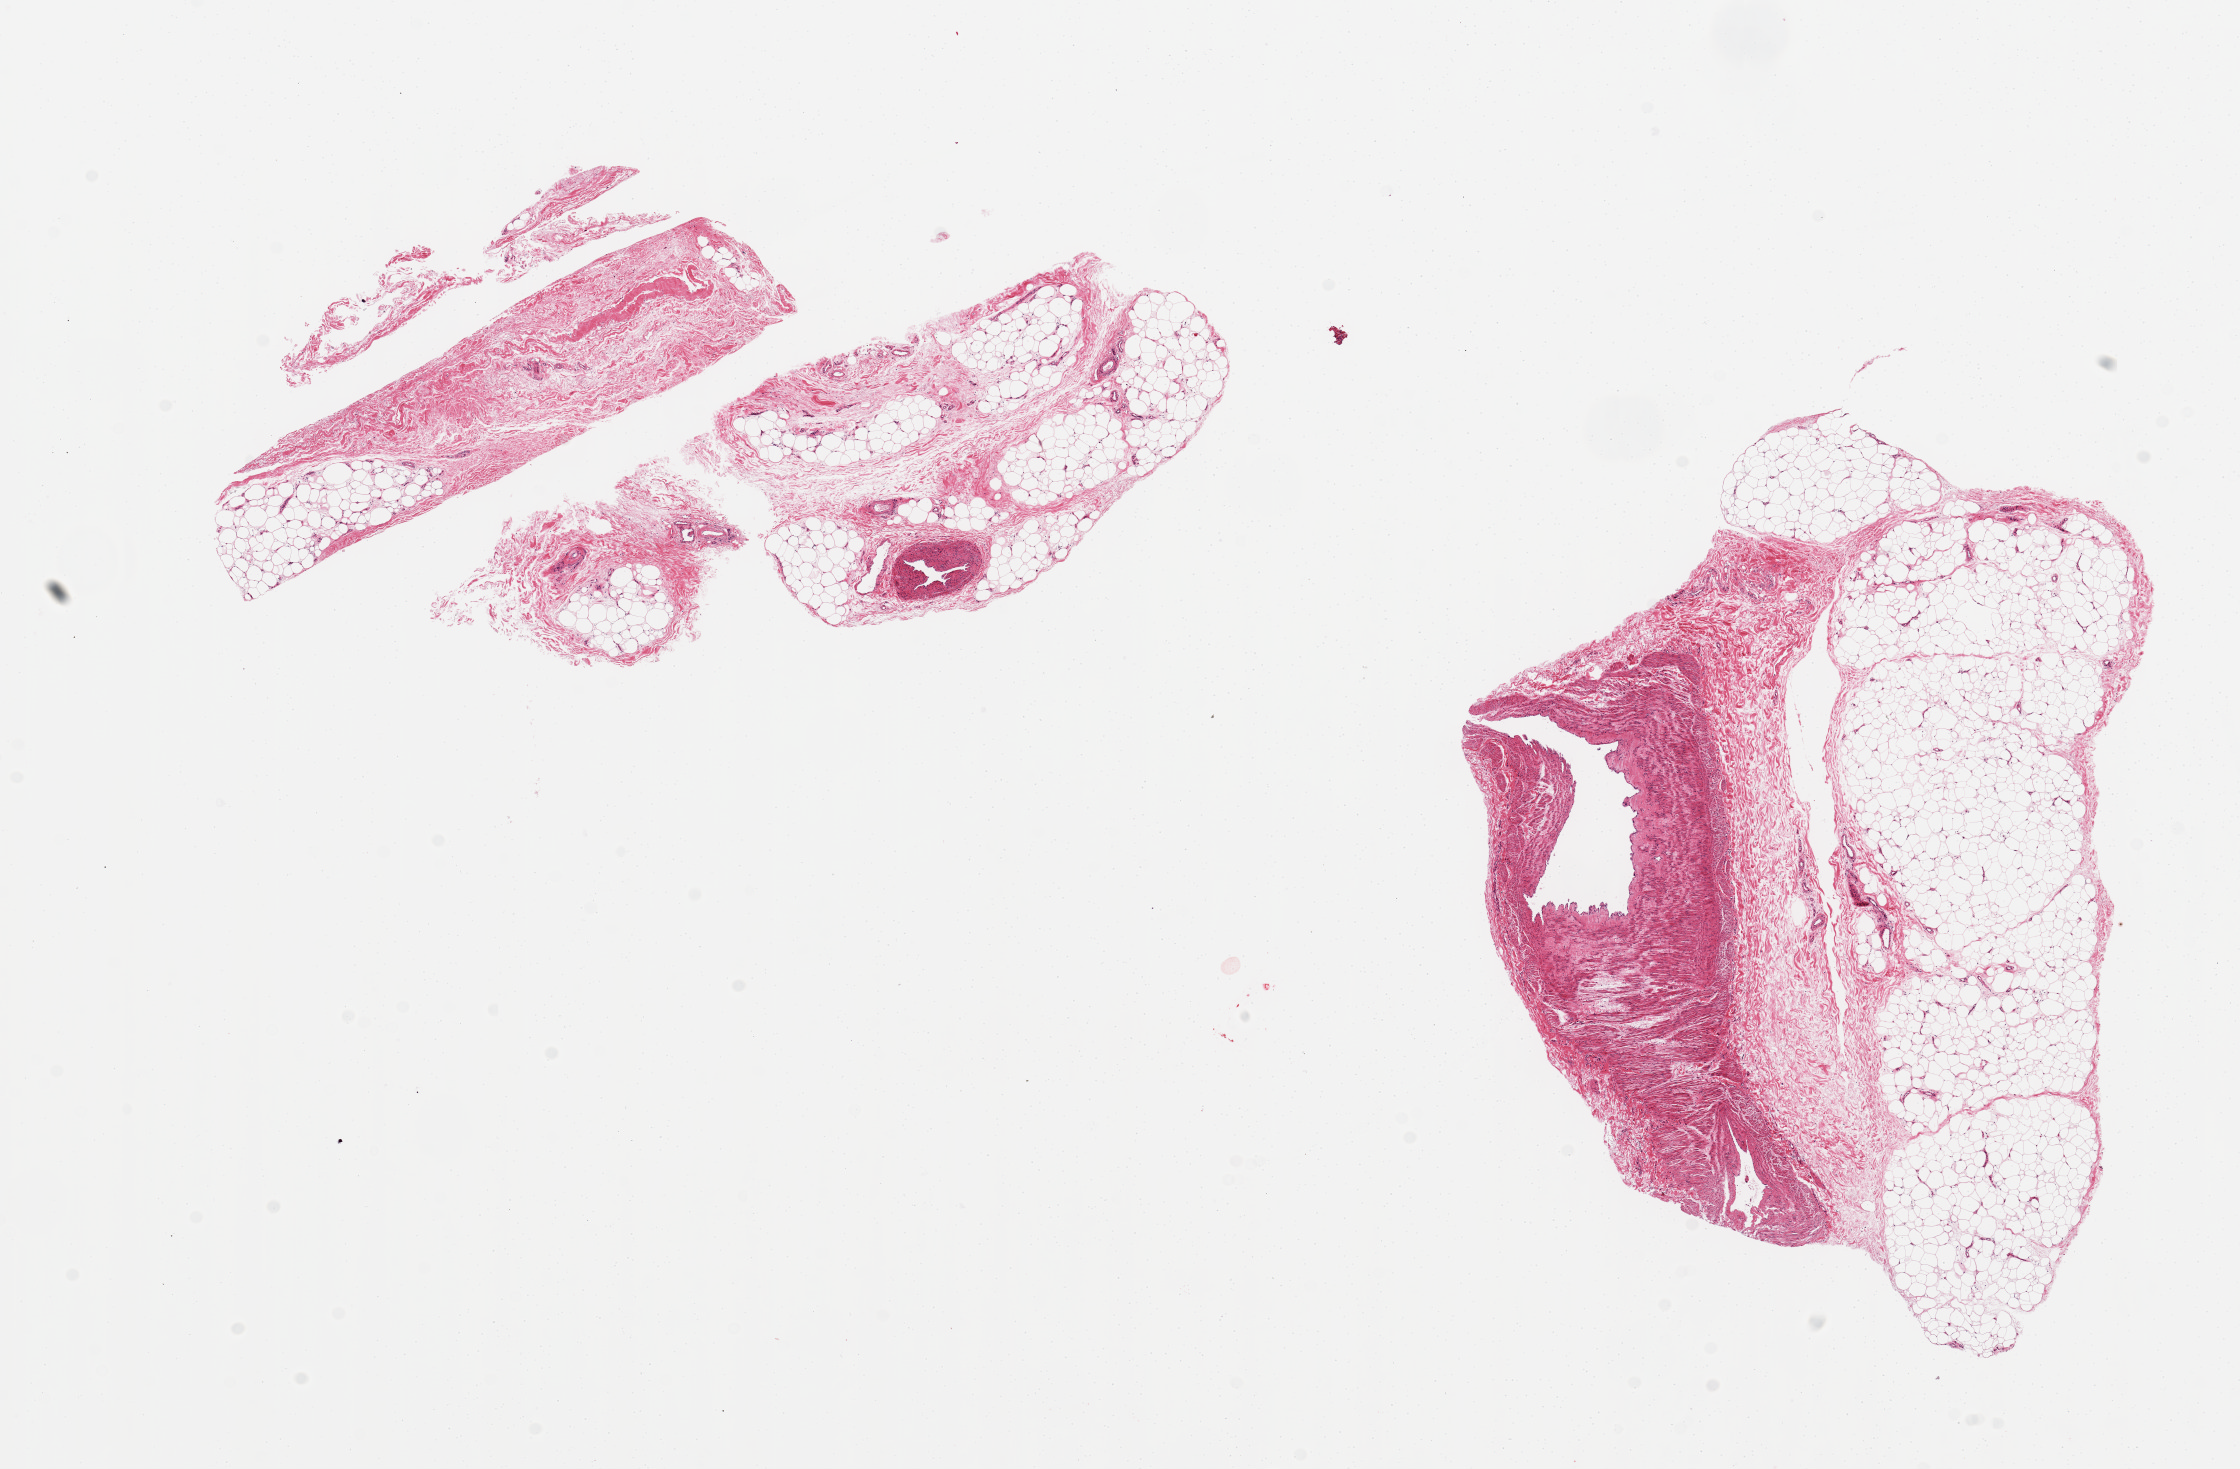
Whole-slide image, hematoxylin and eosin (H&E) stain, brightfield — whole scanned area (about 17.7 x 11.6 mm, acquisition: 20x scan) shown as a low-resolution overview, PAXgene-fixed paraffin-embedded (PFPE) section, section of adipose tissue (target tissue), donor tissue sample. Donor: male.
Pathologist's review note for this sample: 2 aliquots, ~7x5mm. NOTE: ~50% of one is vessel and fibrous tissue.